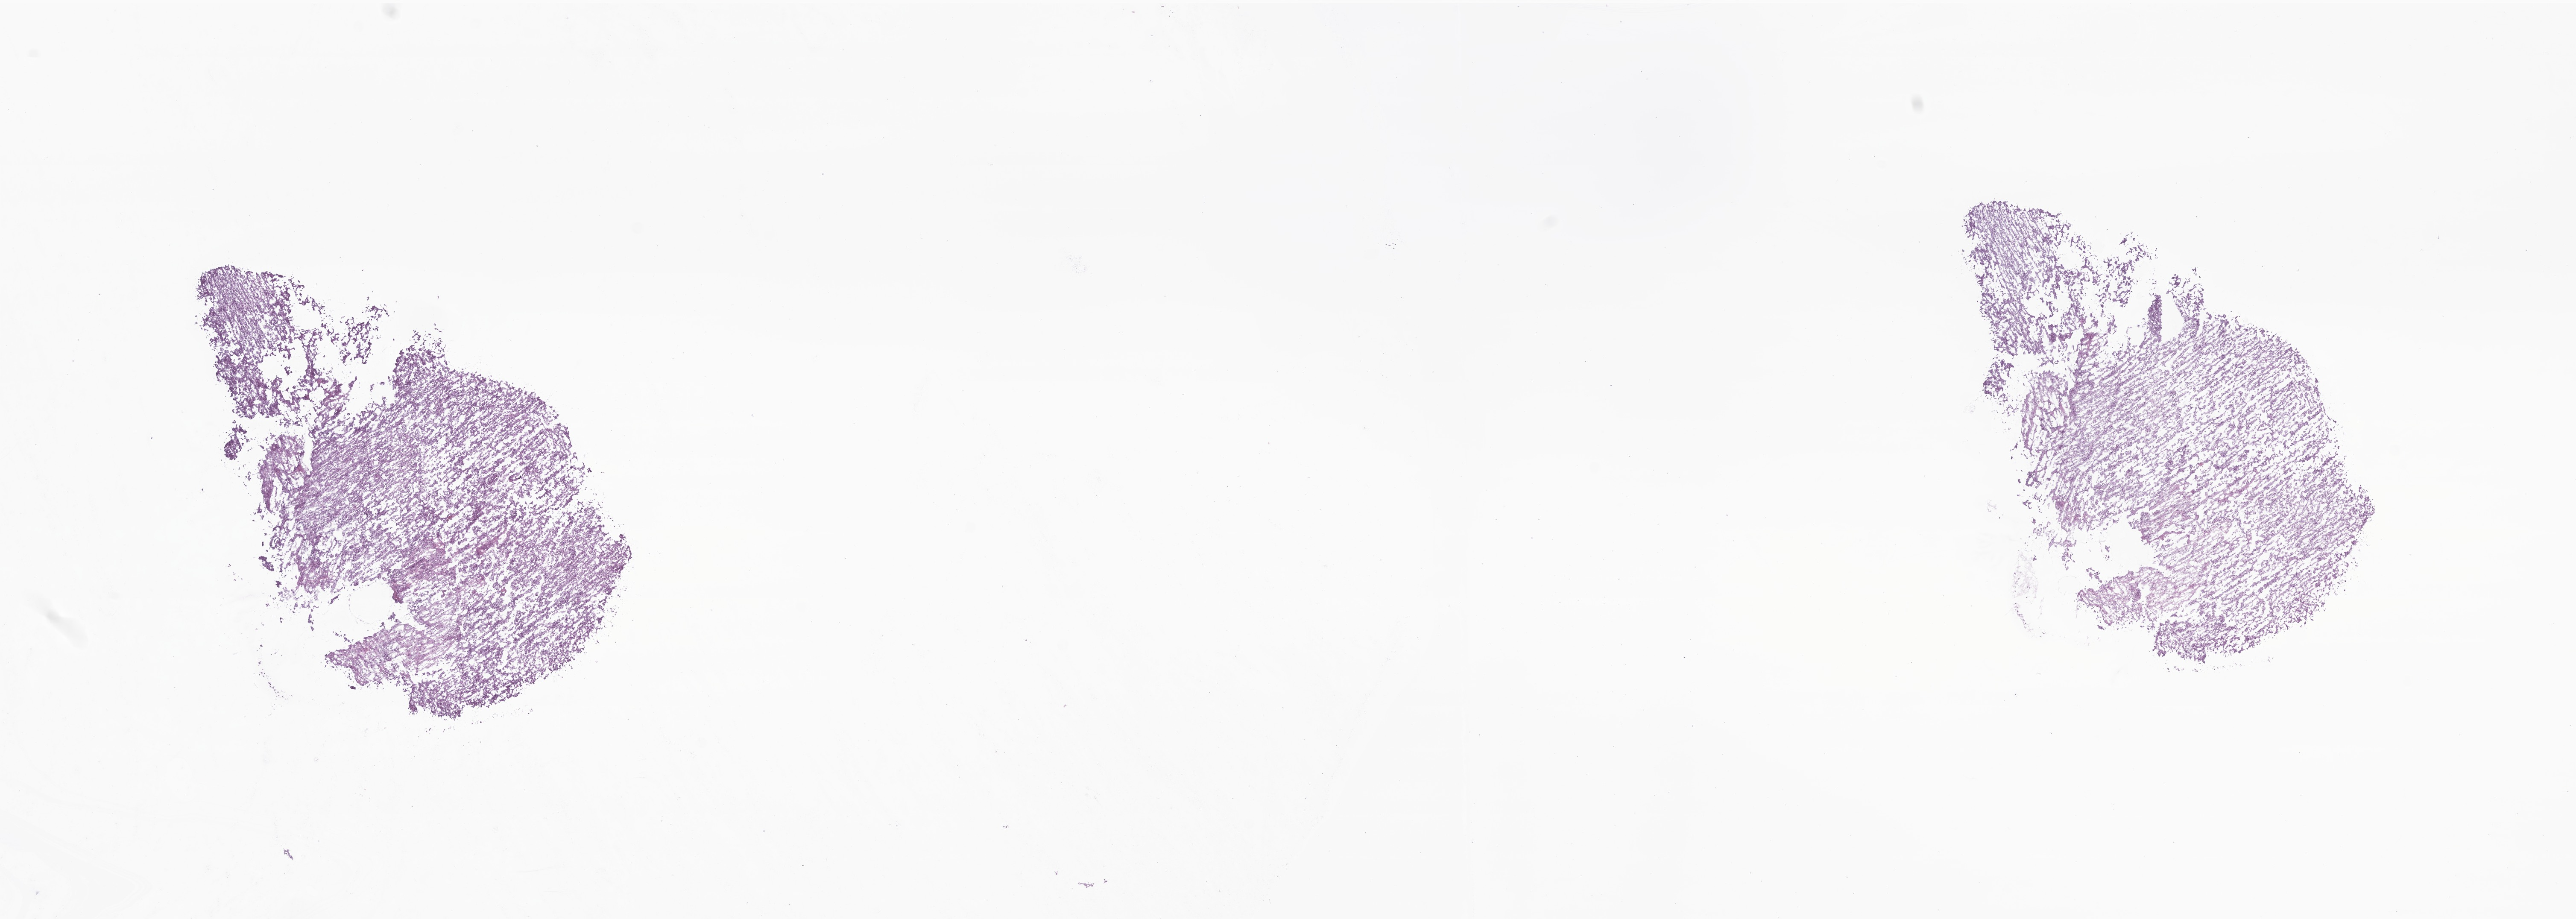
Digitized hematoxylin and eosin (H&E)-stained section of tumor tissue from the temporal lobe — shown as a low-resolution overview of the whole scanned area (about 25.4 x 9.1 mm); frozen section (OCT-embedded). Patient: male, age 716 days (about 2.0 years).
Diagnosis: Atypical teratoid/rhabdoid tumor.